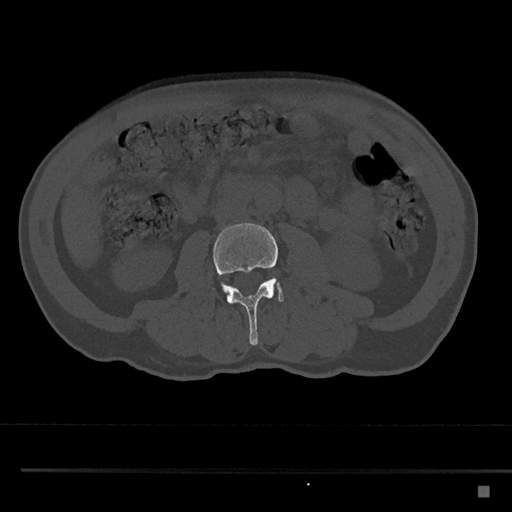
CT including the spine, one axial slice; slice 689 of 797 in the series (ordered by position); reconstruction kernel Br40s/3; bone window (W 1800 / L 400 HU); 0.5 mm slice thickness; 512 × 512 image matrix, field of view 391 × 391 mm. Male patient, age 59 years. Case-level facts recorded for this patient, not image findings: primary cancer: prostate.
Annotated regions visible in this slice (semi-automatic segmentation, software-assisted and operator-edited):
- L3 vertebra: box from (x=212, y=223) to (x=281, y=345) px
- L4 vertebra: (x=226, y=278)–(x=284, y=302)